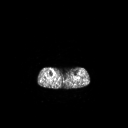
FDG PET of an extremity soft-tissue mass (from a PET/CT study), one axial slice; position 129 of 267 along the scan axis; 3.27 mm slice thickness; 128 × 128 image matrix, field of view 700 × 700 mm. Patient: female, 65 years. Case-level facts recorded for this patient, not image findings: histological type: undifferentiated – high grade; grade: high; site of the primary tumour: right thigh.
Structures marked on this image (expert contour drawn on MRI and transferred to this co-registered scan by the dataset authors):
- gross tumour volume (mass): bounding box [x1, y1, x2, y2] px = [52, 70, 54, 72]